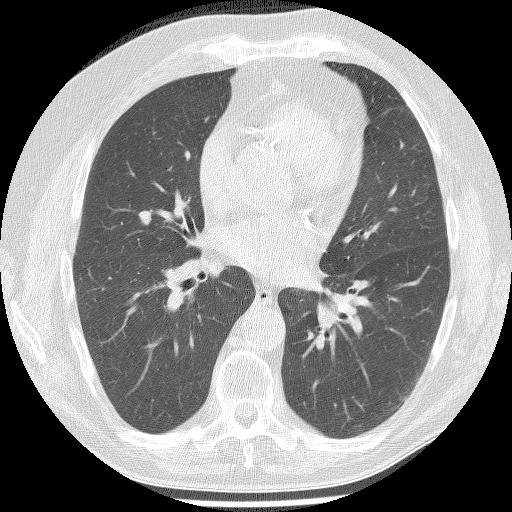
Low-dose screening chest CT, axial slice; second annual screen; lung window (W 1500 / L -600 HU); lung (sharp) reconstruction kernel (BONE); 512 × 512 image matrix. Male participant, aged 61 years at enrolment.
Lesion marked by an expert reader, bounding box [x1, y1, x2, y2] px = [121, 197, 158, 237]. The screening reader recorded 2 non-calcified nodules or masses ≥4 mm on this exam (right upper lobe, right lower lobe); which of them this box marks is not recorded. Later outcome: lung cancer diagnosed 147 days after this screen — bronchiolo-alveolar adenocarcinoma, NOS, right middle lobe, well differentiated (G1), stage IA (AJCC 6th edition), 15 mm at pathology.